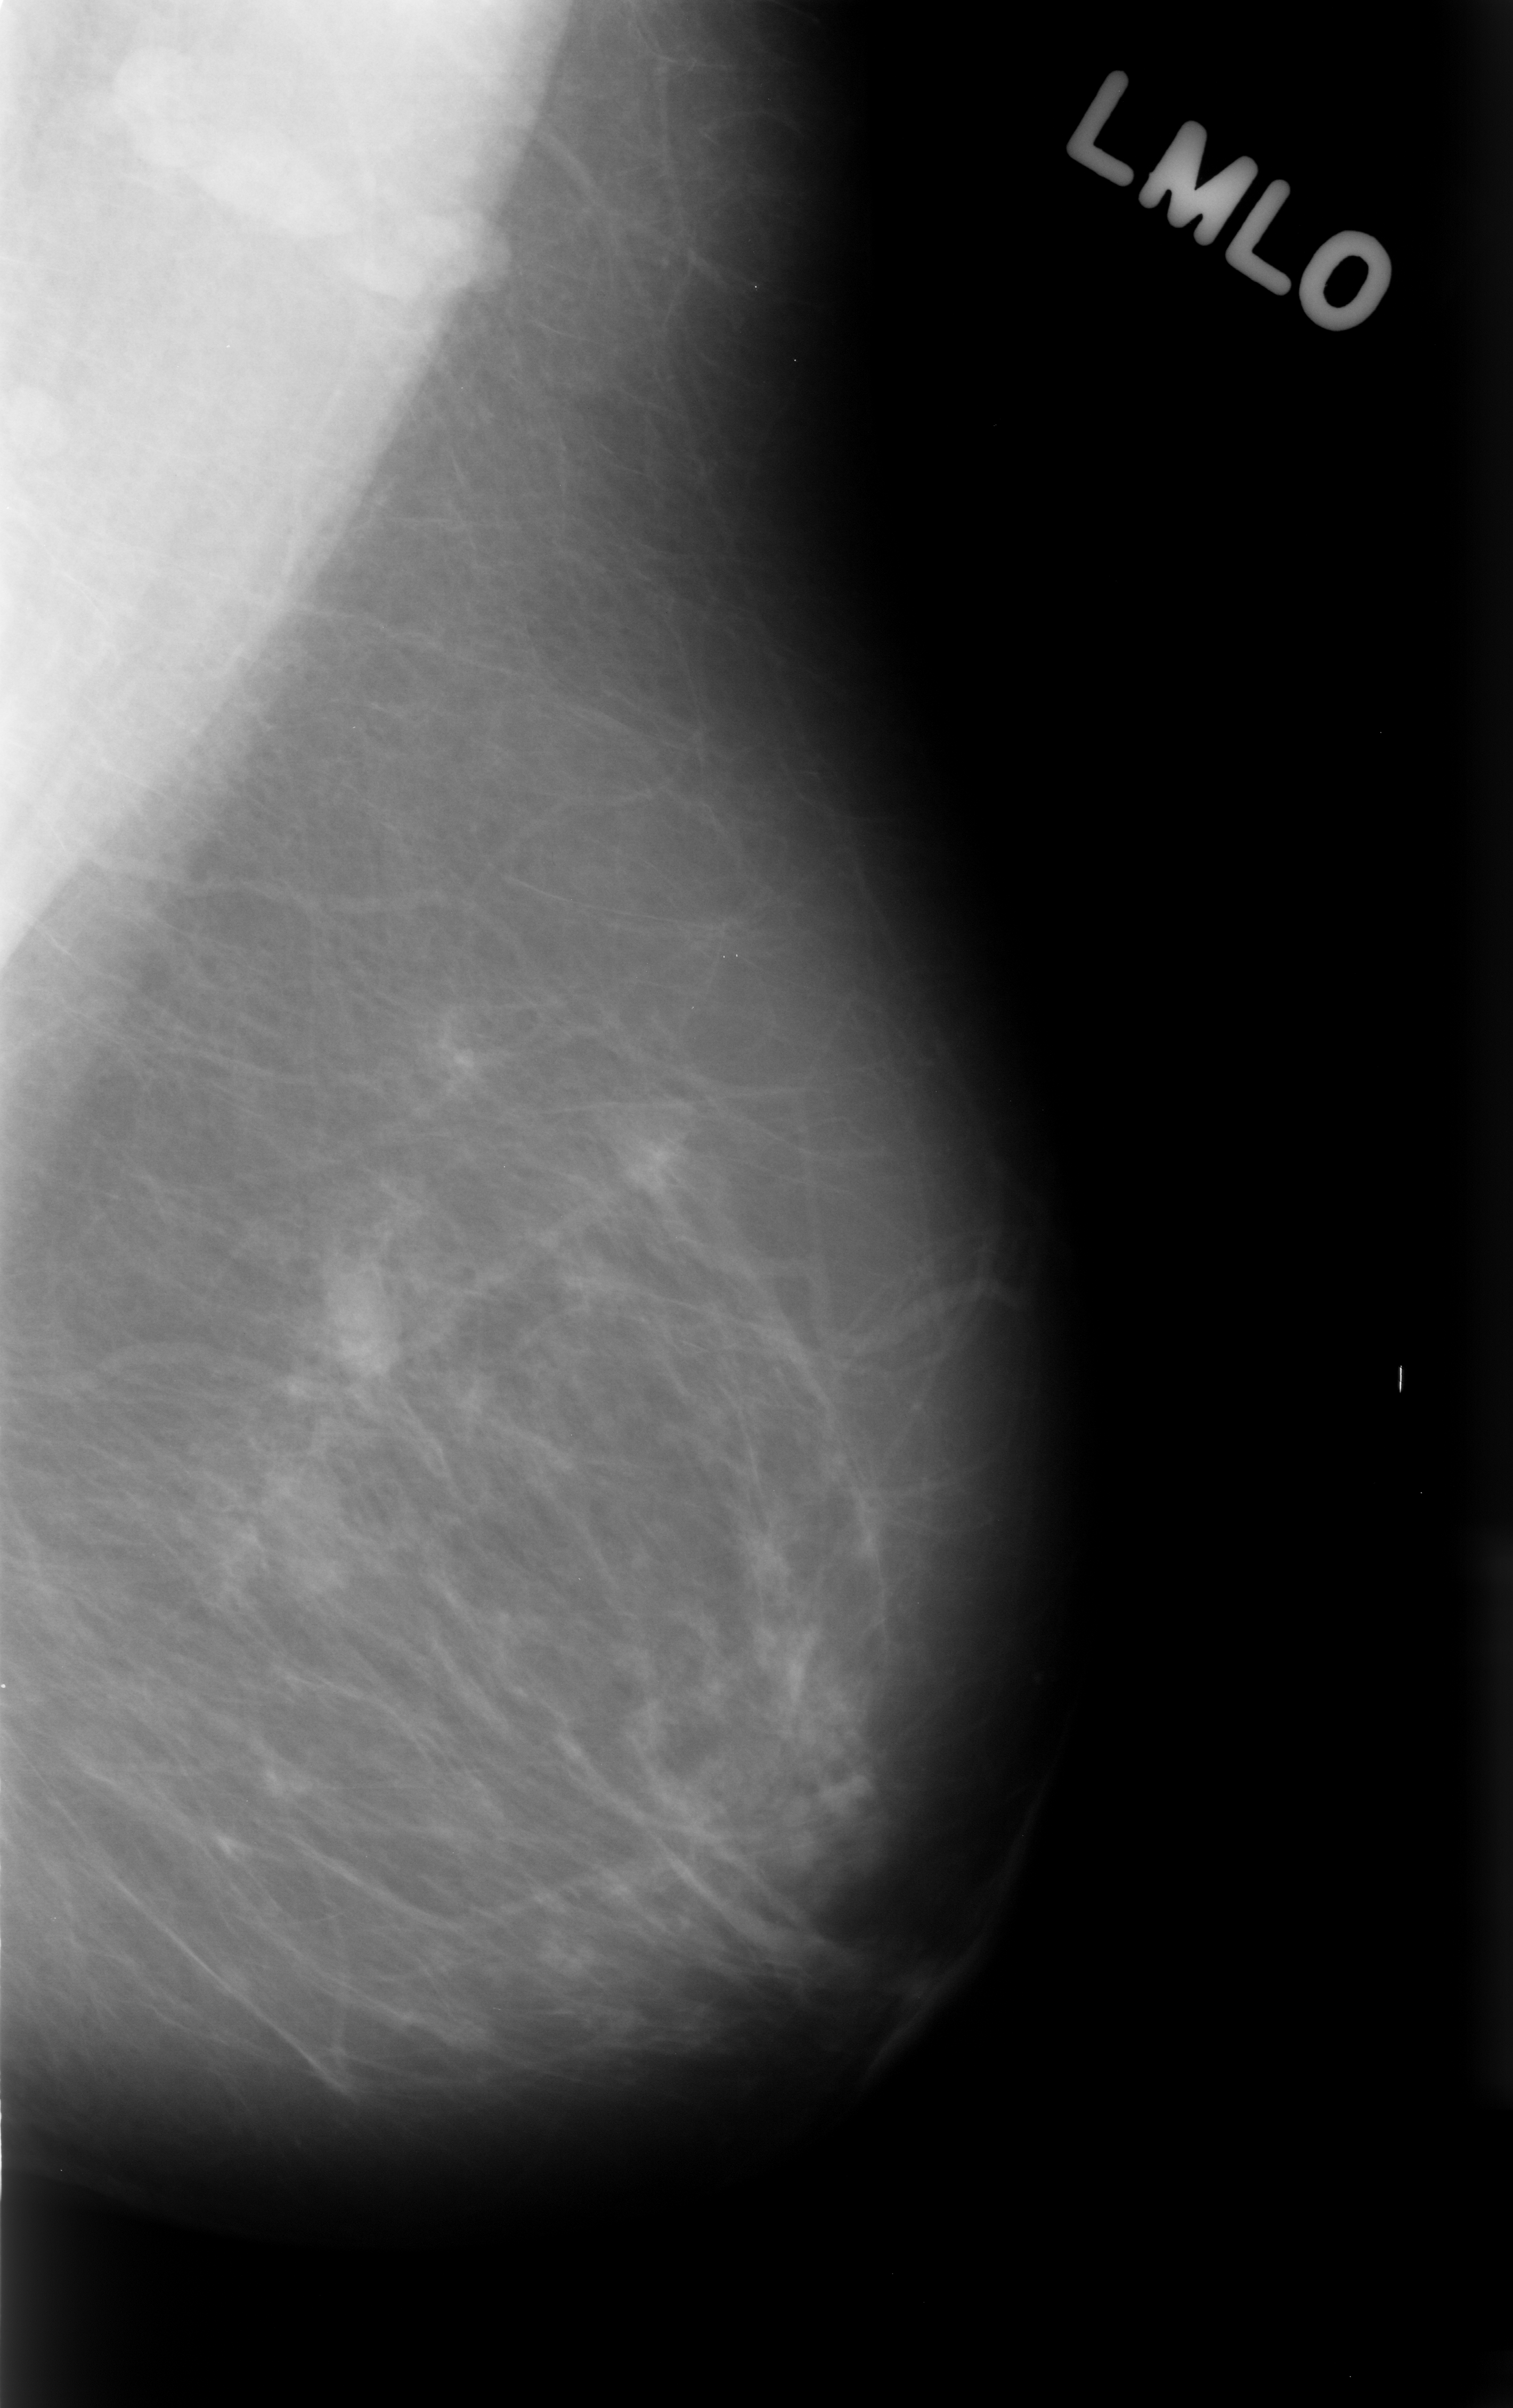
Scanned film-screen mammogram; left breast; MLO view; breast composition: almost entirely fatty (BI-RADS density category 1 of 4).
Finding: mass, shape oval, margins circumscribed; BI-RADS assessment category 3; subtlety rating 5 on a 1 (subtle) to 5 (obvious) scale; benign without callback (not worked up further).